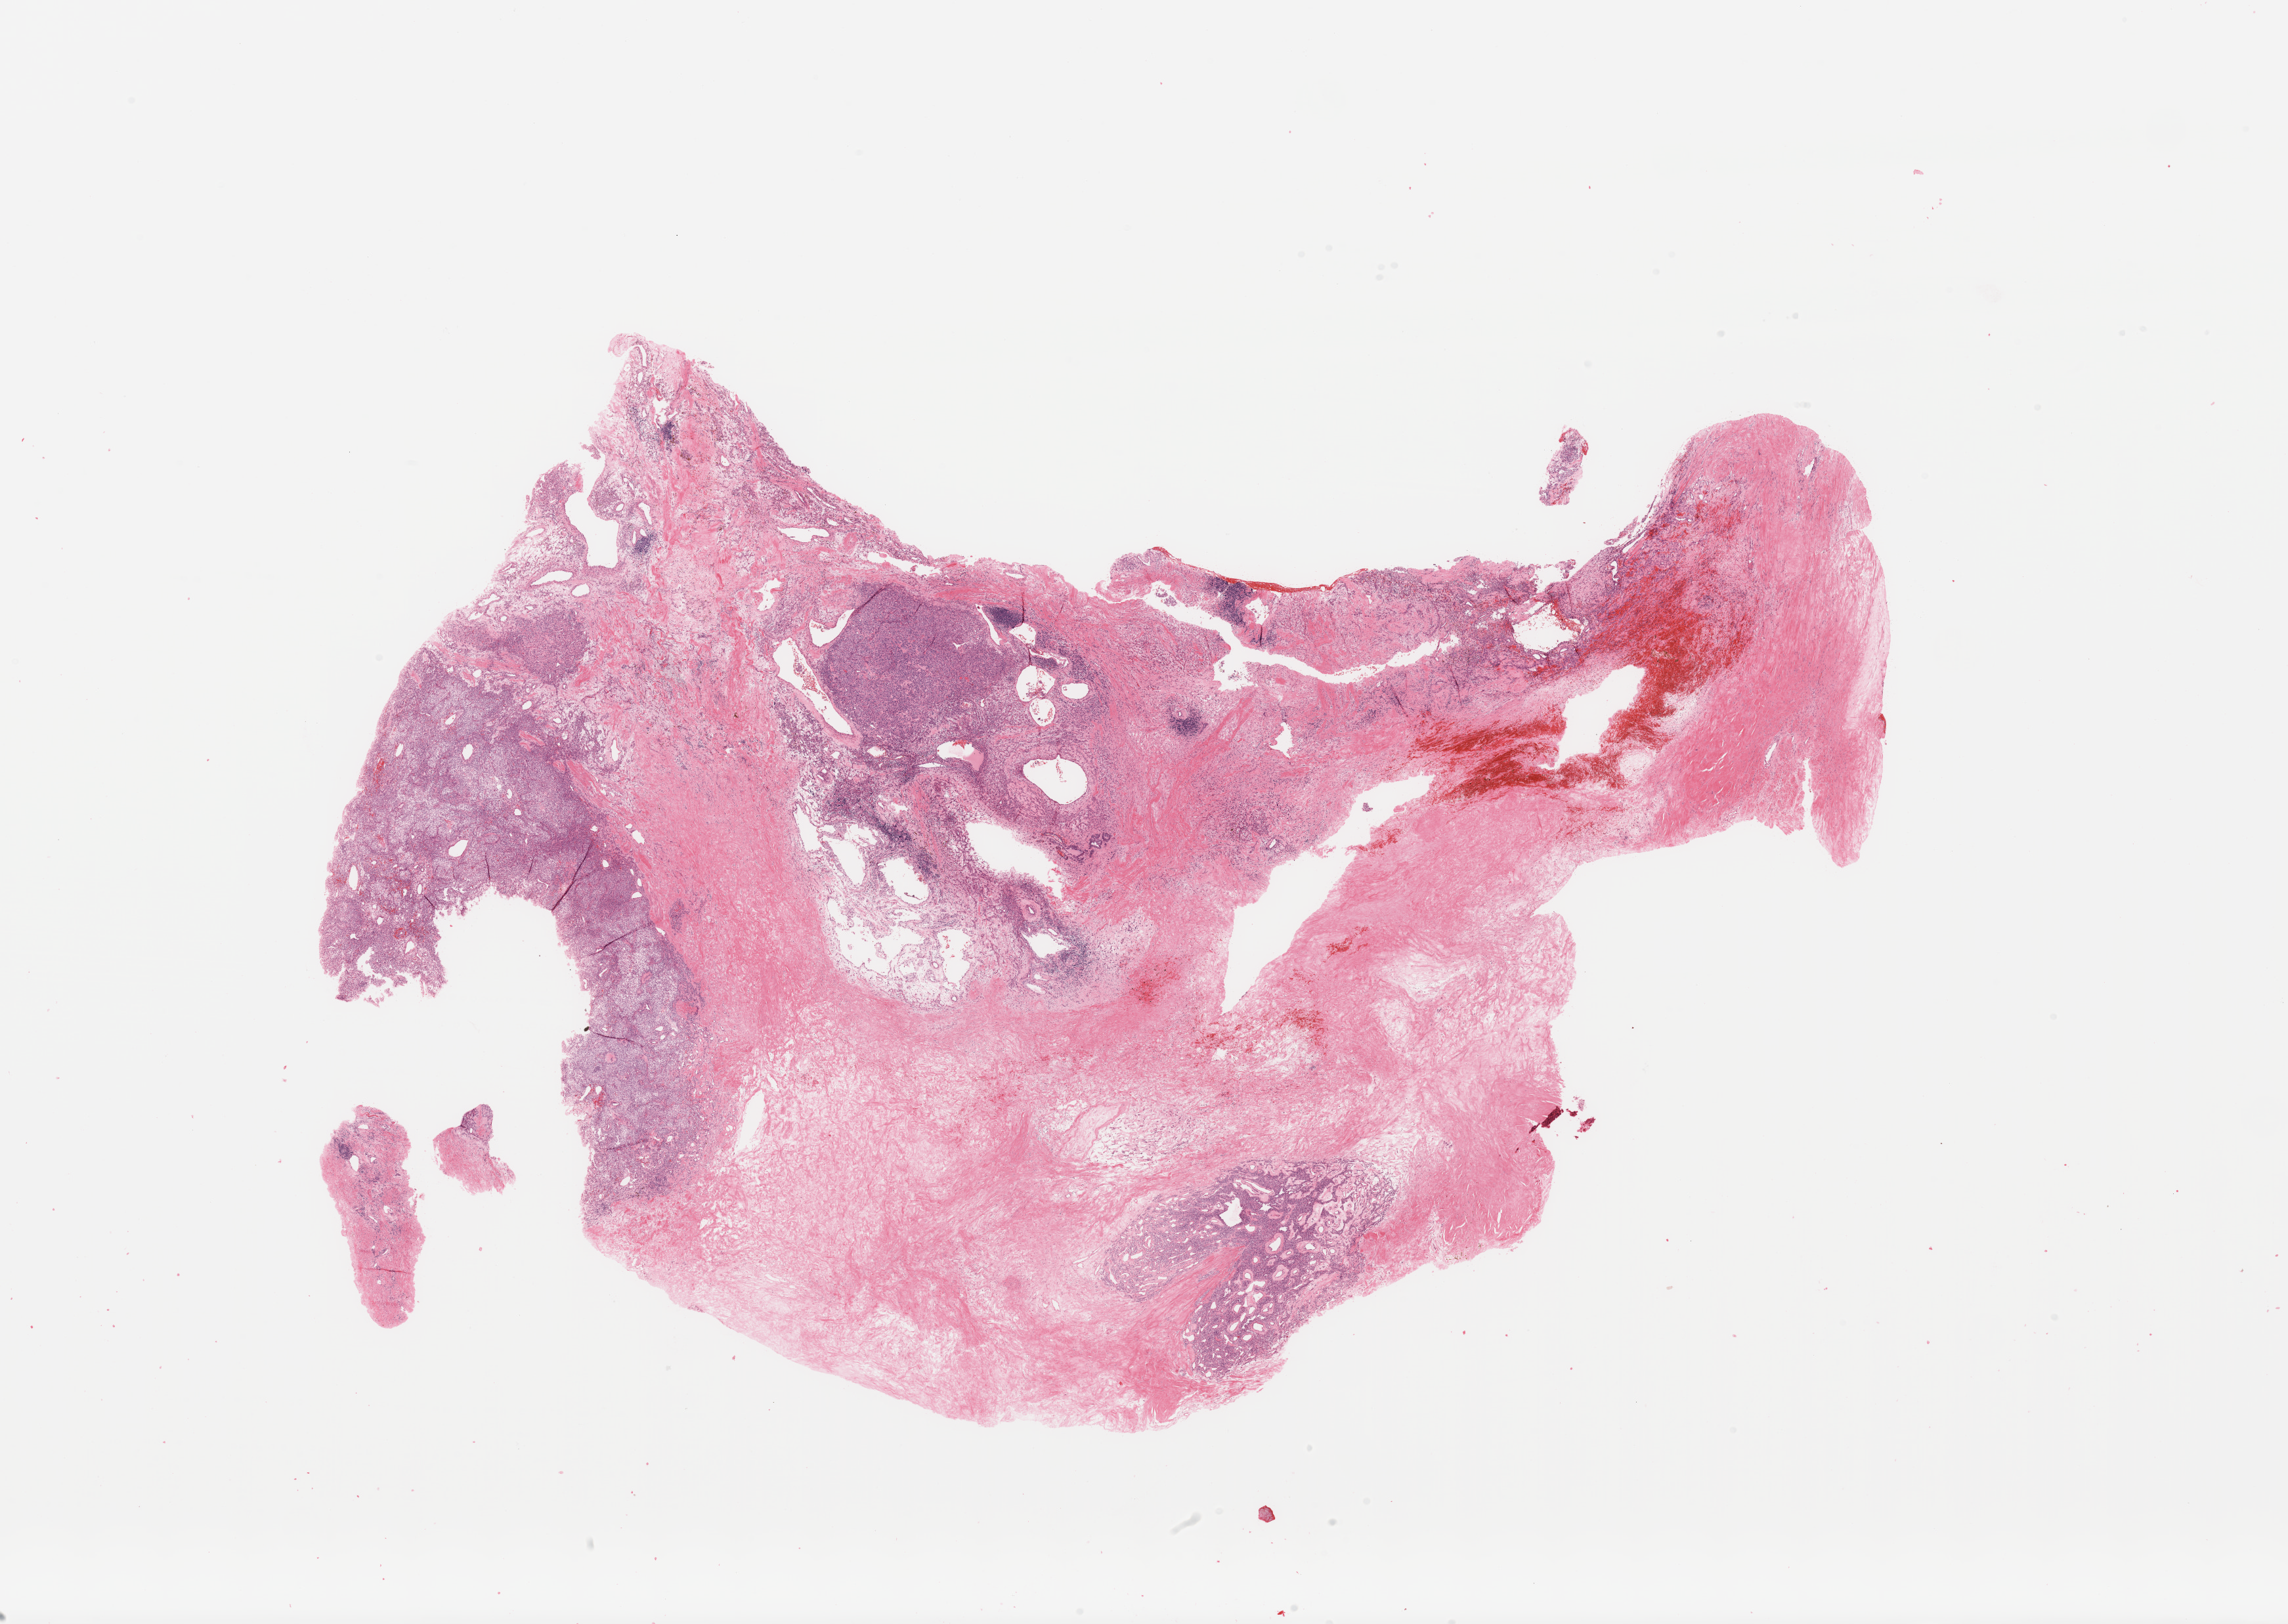
Digitized H&E-stained tissue section (whole slide), whole scanned area (about 27.6 x 19.6 mm, from a 20x scan) shown as a low-resolution overview. Tumour tissue sample, sampled site: kidney. Male, 52 y/o.
Histologic diagnosis: Renal cell carcinoma, NOS.